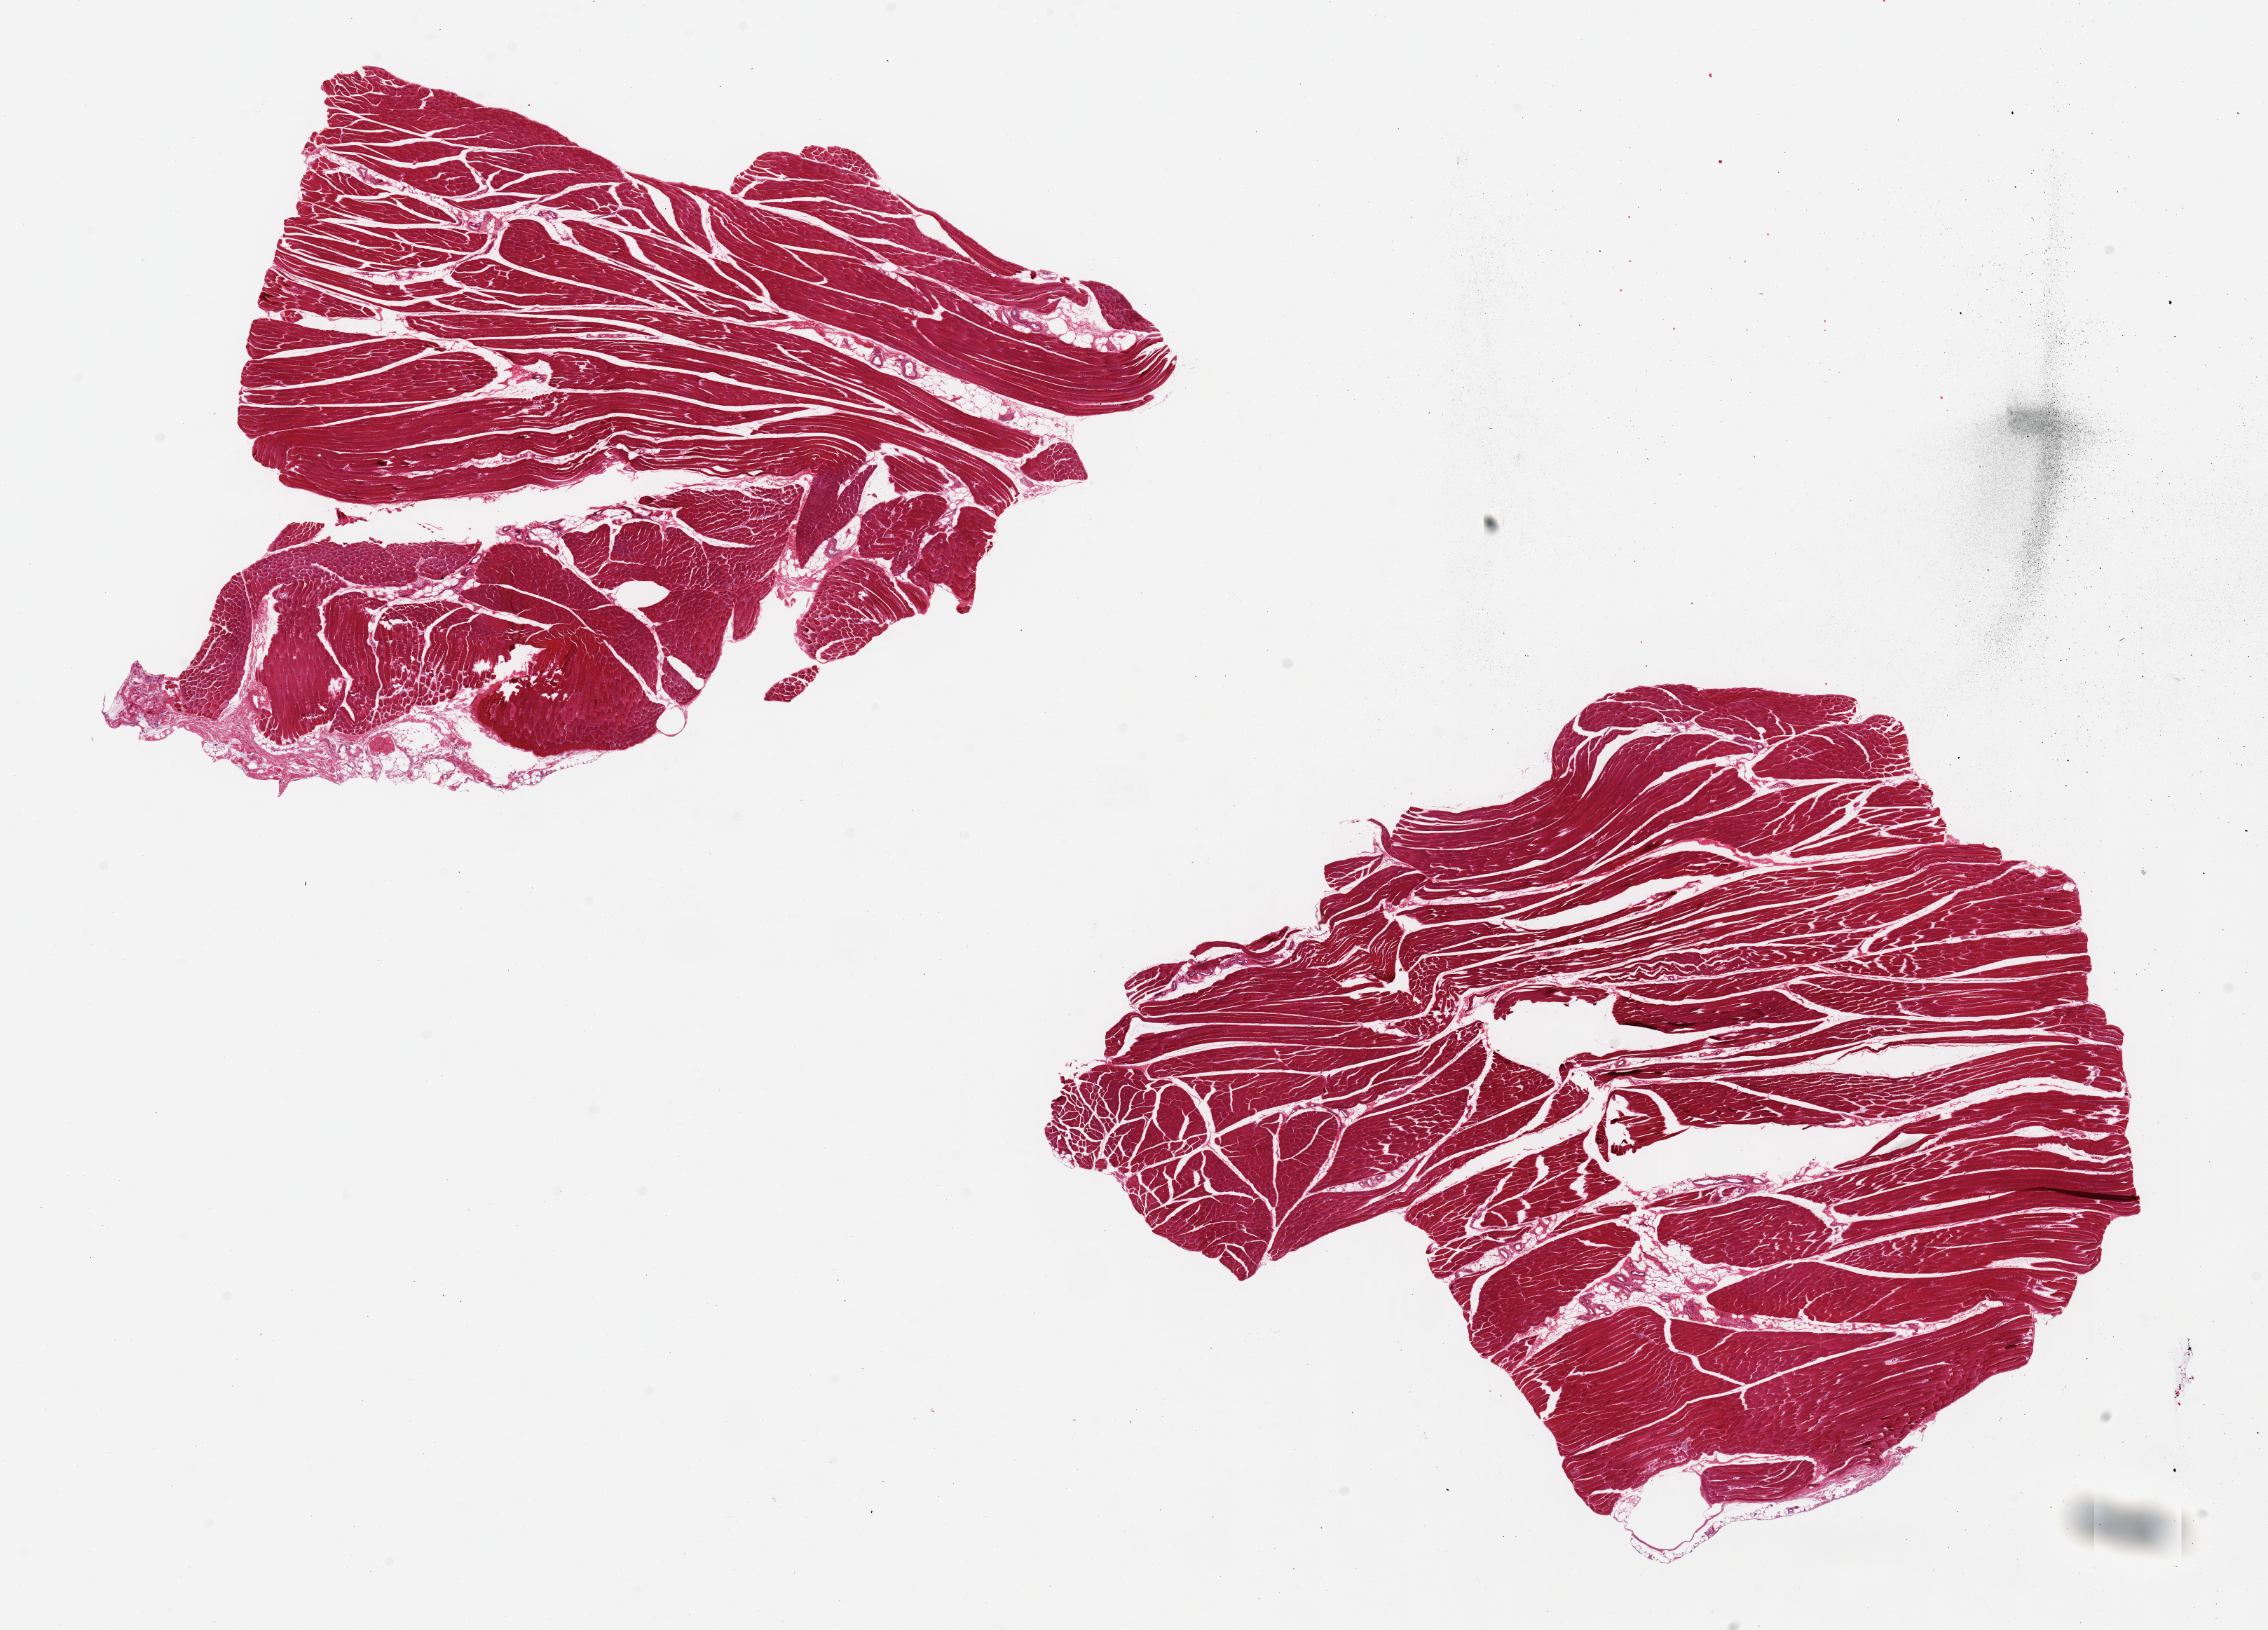
Whole-slide image, H&E stain — whole scanned area (about 25.6 x 18.4 mm, acquisition: 20x scan) shown as a low-resolution overview, PAXgene-fixed, paraffin-embedded tissue, target tissue: skeletal muscle, donor tissue sample. Donor sex: male.
- pathologist's review note for this sample: 2 pieces, 12x8 & 11x9.5mm; ~10% interstital fat